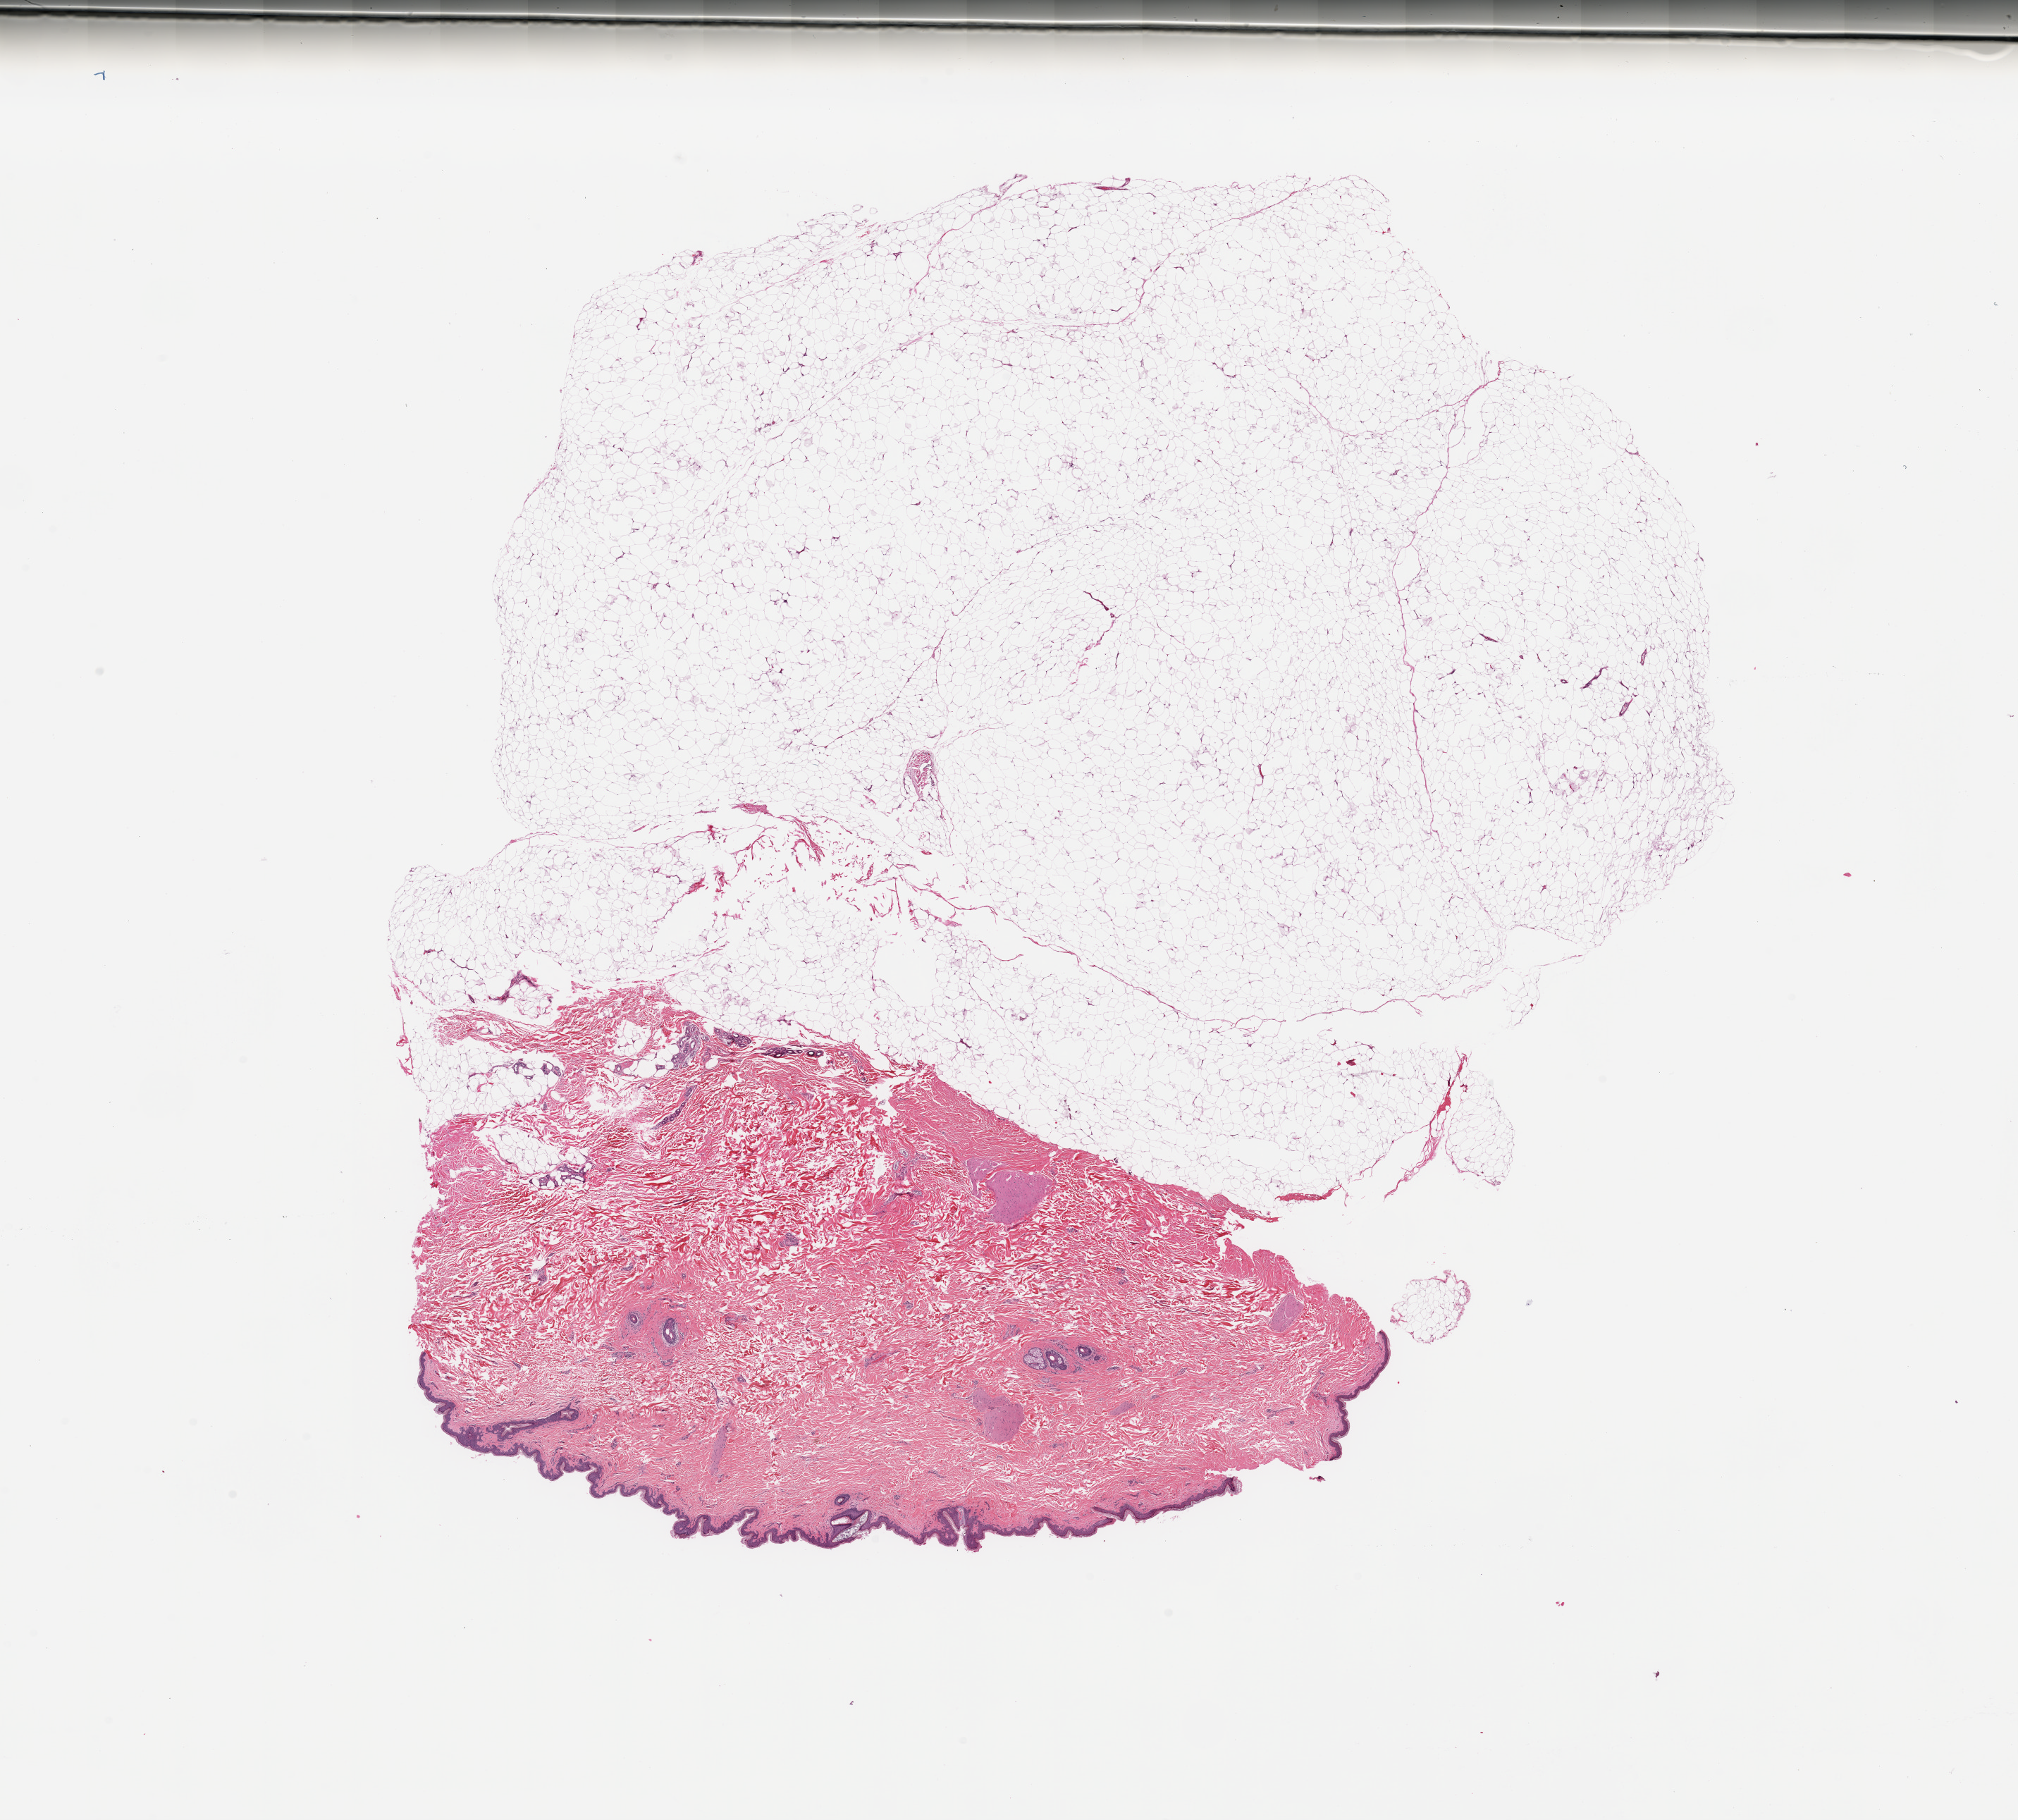
Digitized Hematoxylin and eosin (H&E) stained tissue section (whole slide), a low-resolution overview of the entire scanned area, about 22.6 x 20.4 mm; normal (non-tumour) tissue sample, sampled site: trunk. 69-year-old female patient.
This section: normal (non-tumour) tissue from the same patient. Patient diagnosis: Malignant melanoma, NOS.